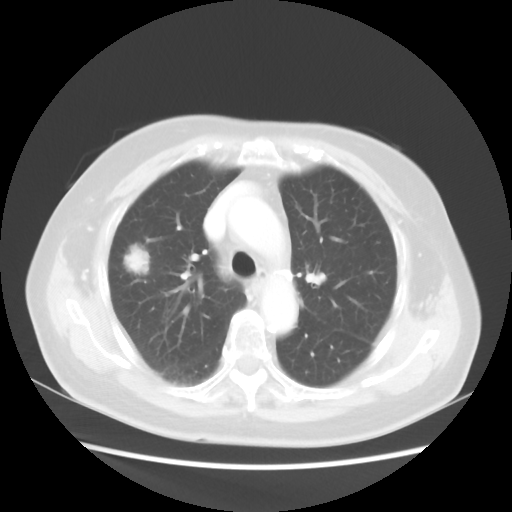
Chest CT, one axial slice; 100 kVp; lung window (W 1500 / L -600 HU); 512 × 512 image matrix. Patient: female, 75 years. From the clinical record (not read from this slice): clinical TNM (as recorded): T1c N0 M0.
Annotated regions visible in this slice (rectangle marked by the reading radiologist):
- lung tumour (recorded histology: adenocarcinoma): bounding box <125,242,152,279> (left, top, right, bottom; pixels)